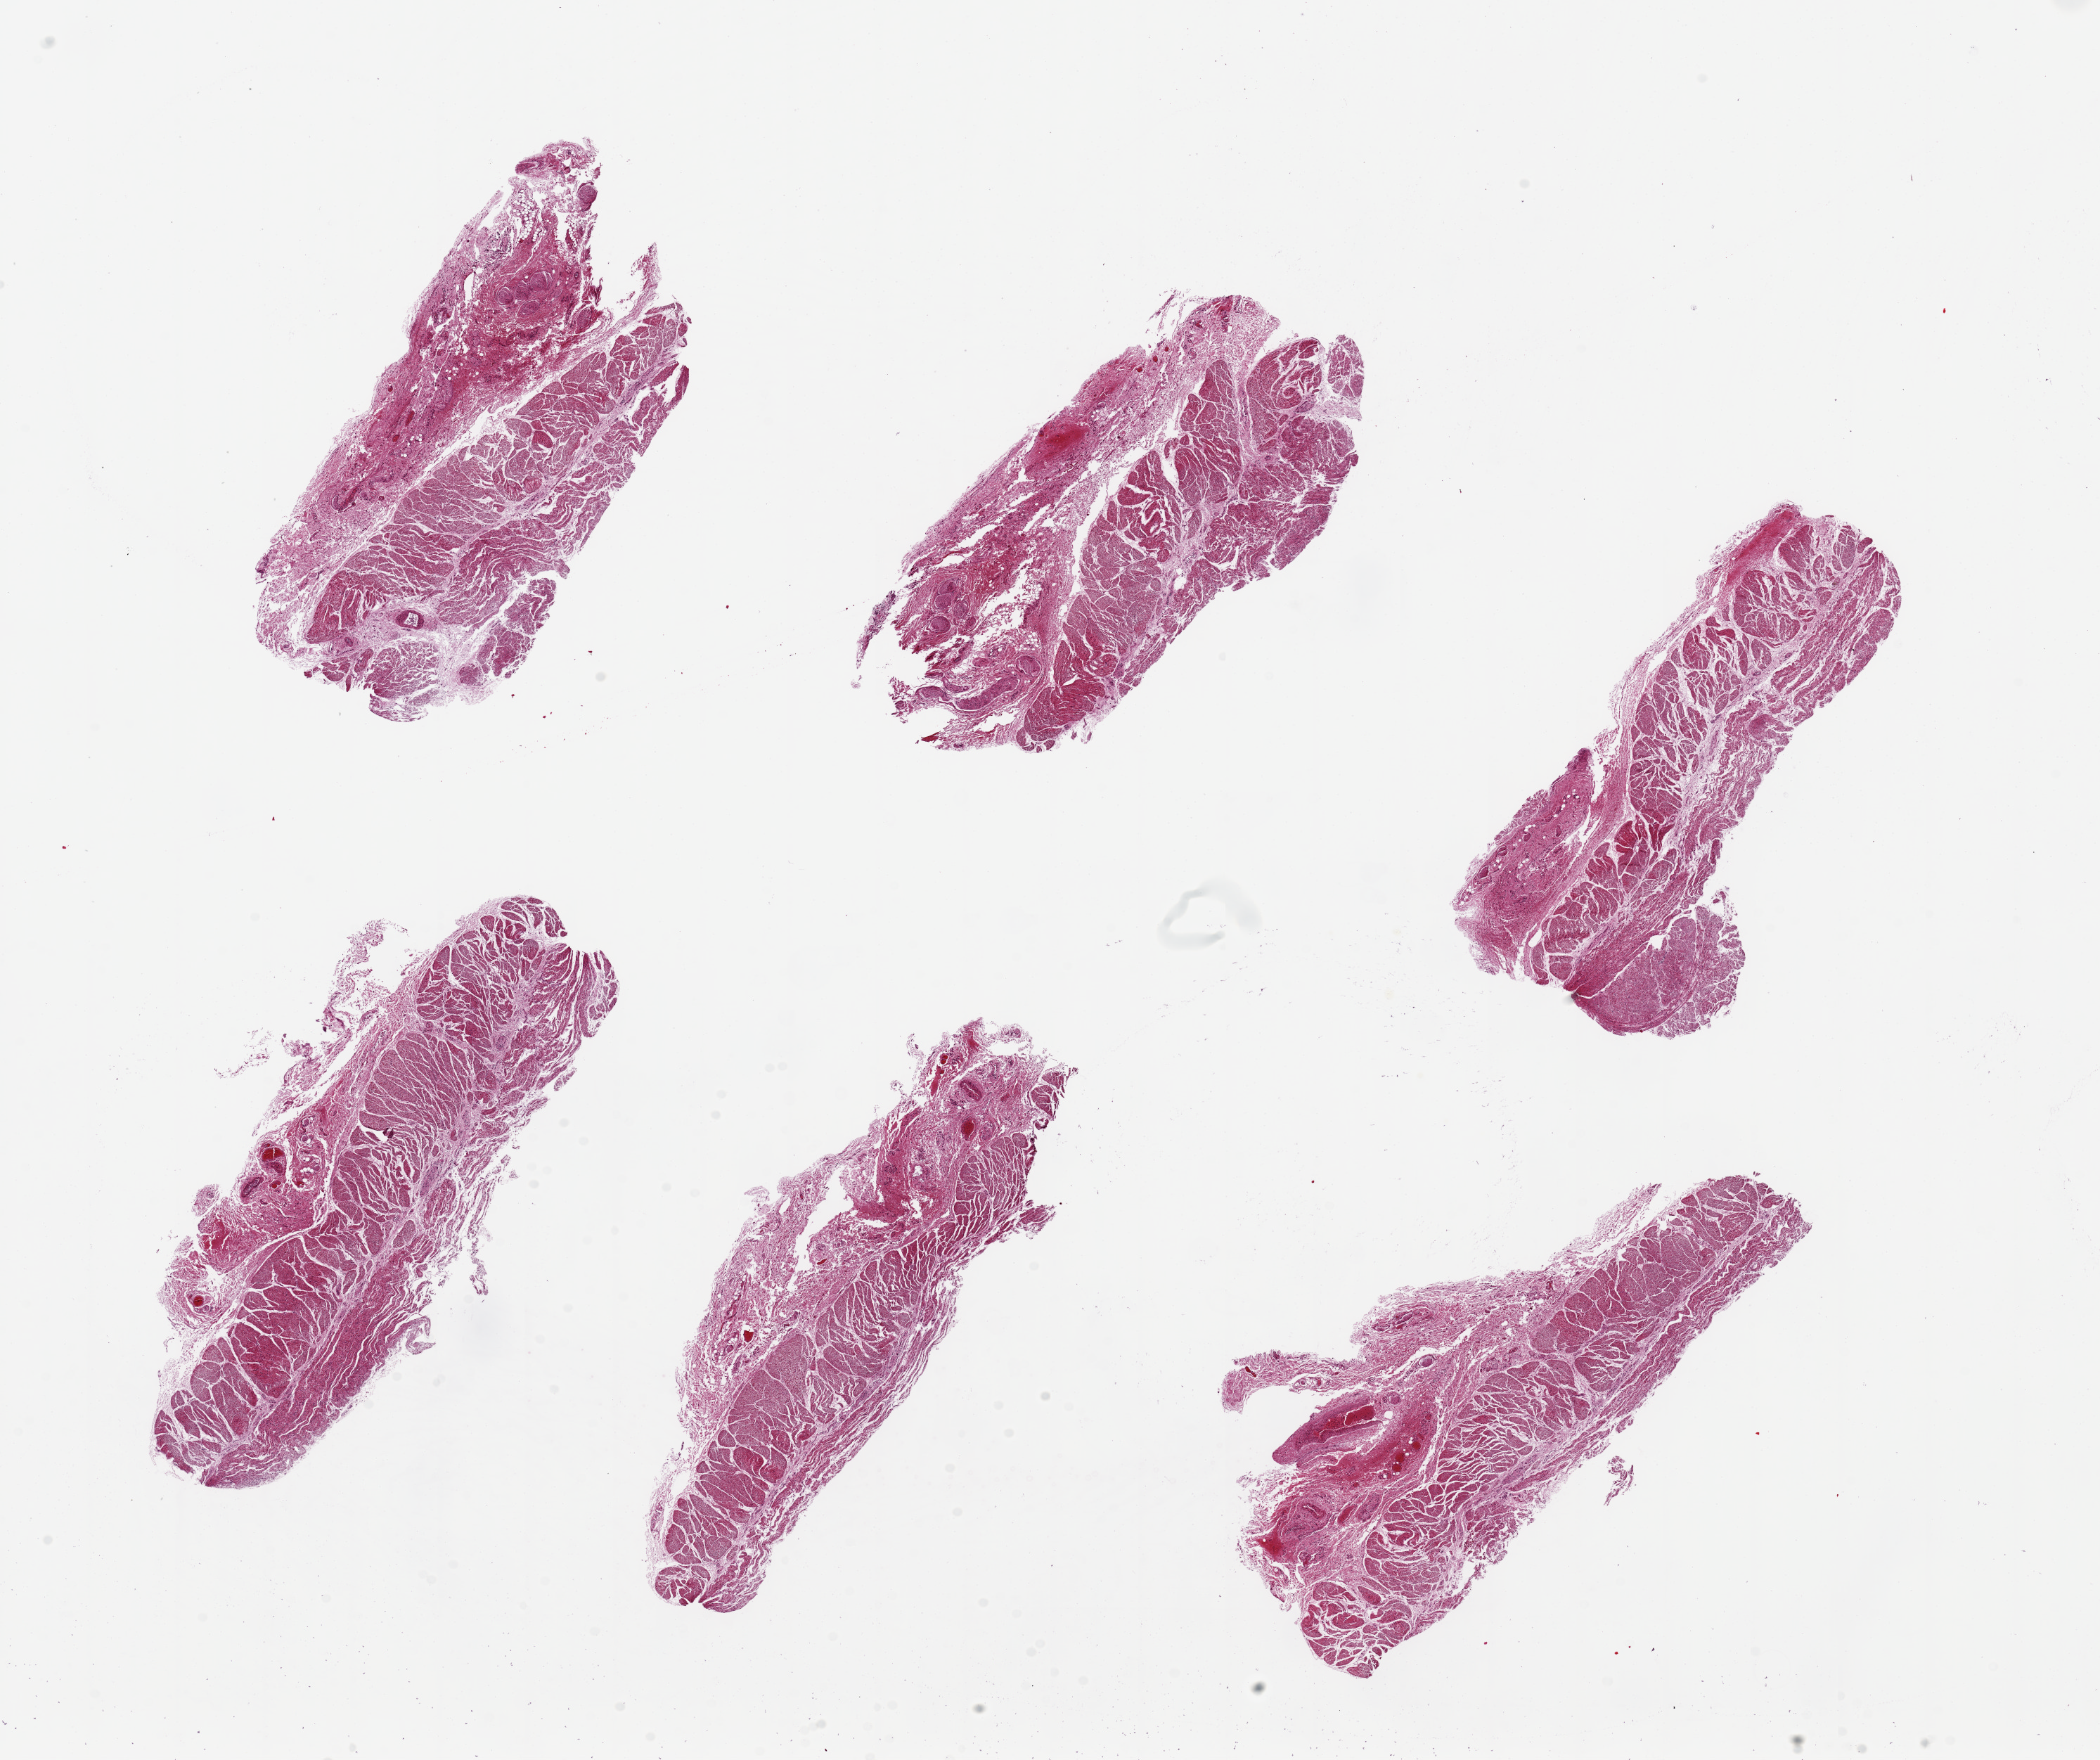
Whole-slide image, haematoxylin and eosin stain, a low-resolution overview of the entire scanned area, about 23.6 x 19.8 mm (acquisition: 20x scan). PAXgene-fixed, paraffin-embedded tissue. Target tissue: esophageal muscle. Tissue donor sample. Donor: female.
Review note (as recorded): 6 pieces ~7x3mm, all muscularis.